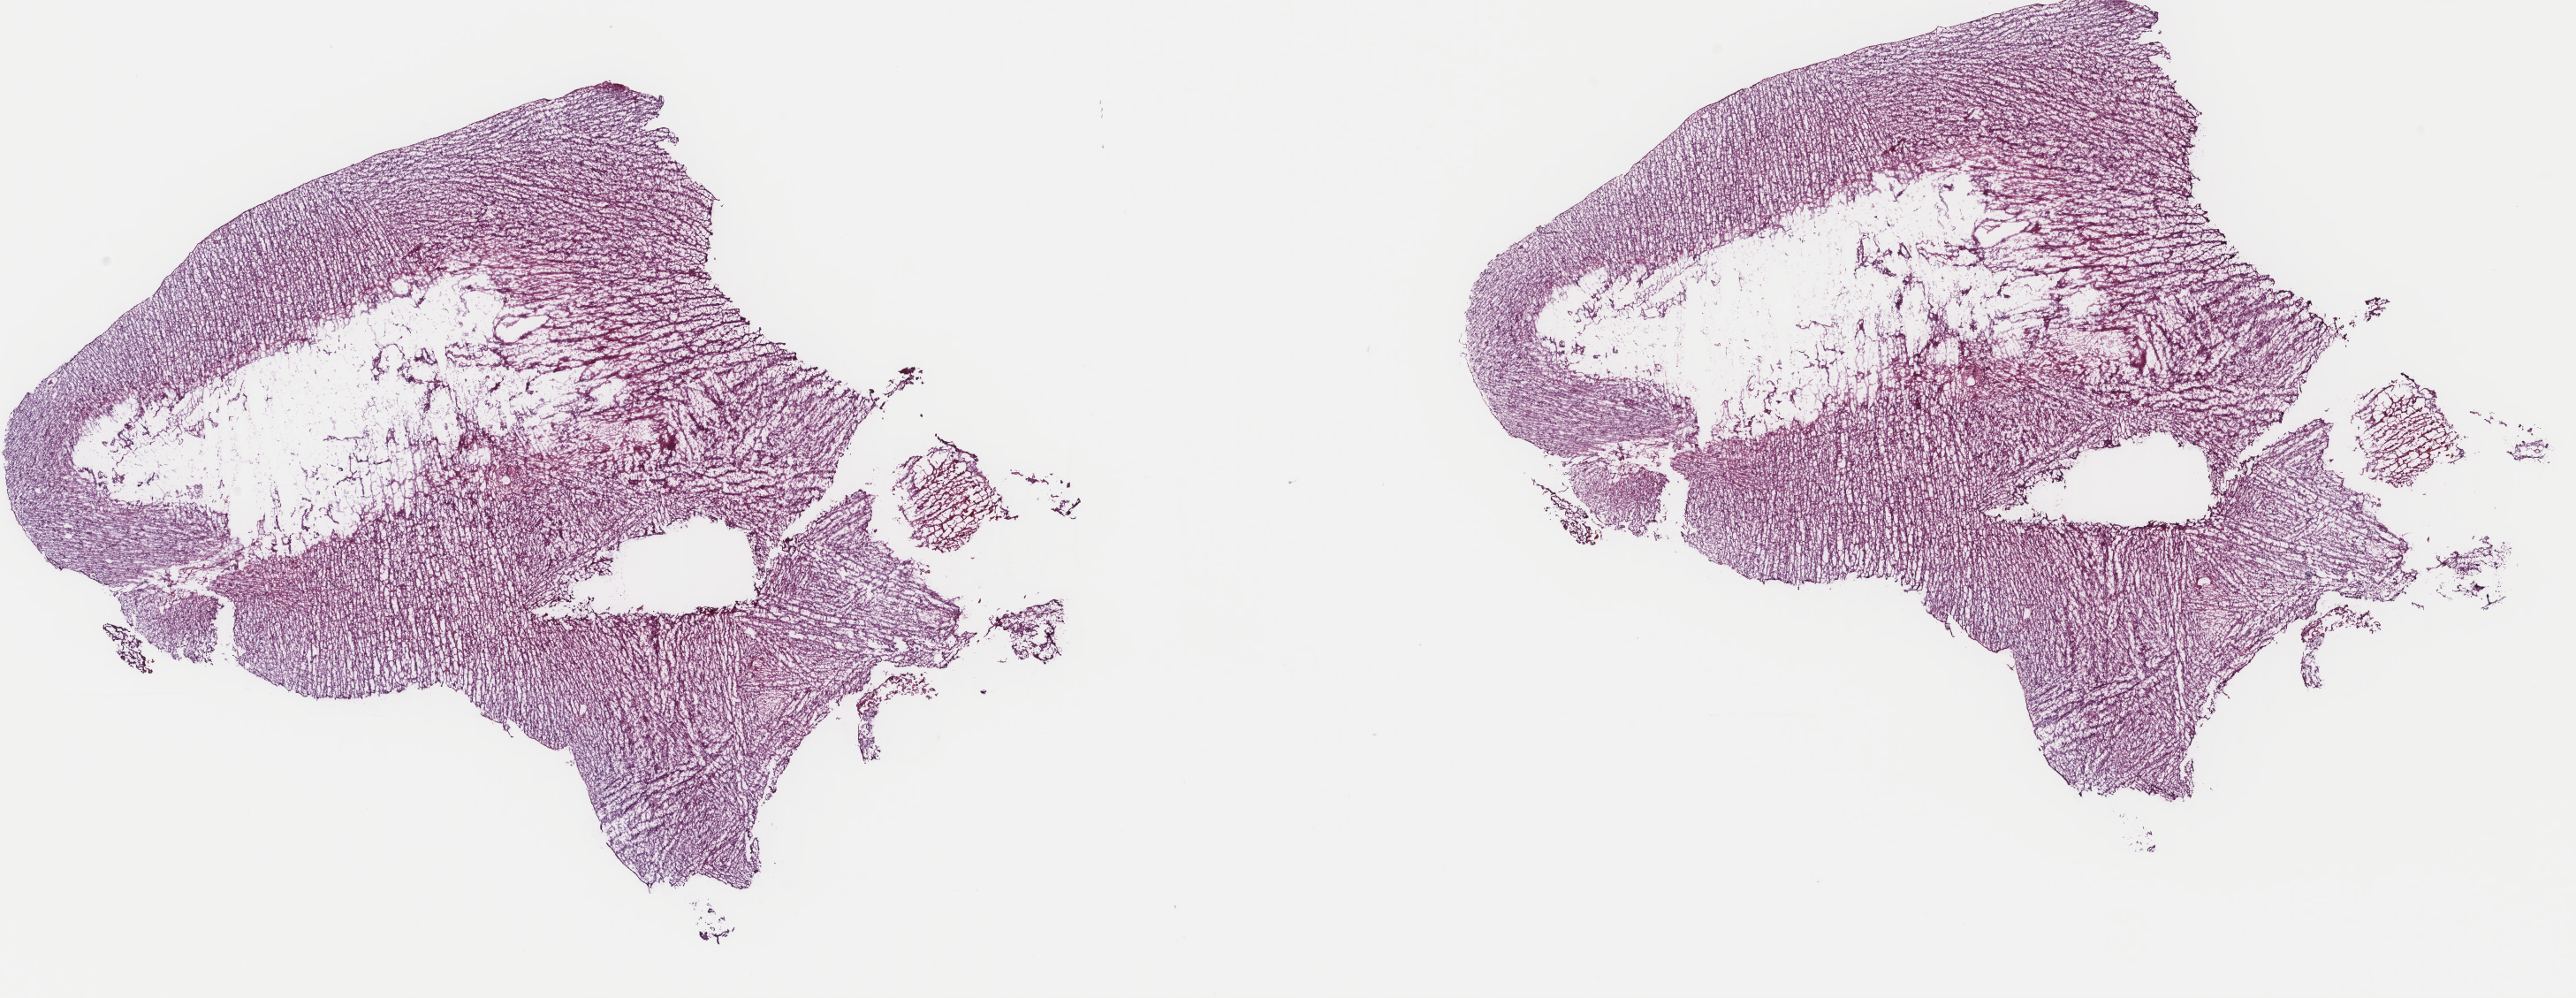
Digitized H&E tissue section (whole slide), a low-resolution overview of the entire scanned area, about 23.1 x 9.0 mm; frozen section; brain, primary tumour sample. Male patient; age at initial diagnosis 21 years. Histologic grade: G3 (poorly differentiated). Composition of this section per pathologist review: tumour cells 40%, tumour nuclei 80%, normal cells 10%, stromal cells 50%, necrosis 0%. Infiltration values recorded for this section: lymphocyte infiltration 0%, monocyte infiltration 0%, neutrophil infiltration 0%.
Laterality: left. Histologic diagnosis: Astrocytoma, anaplastic (cerebrum).